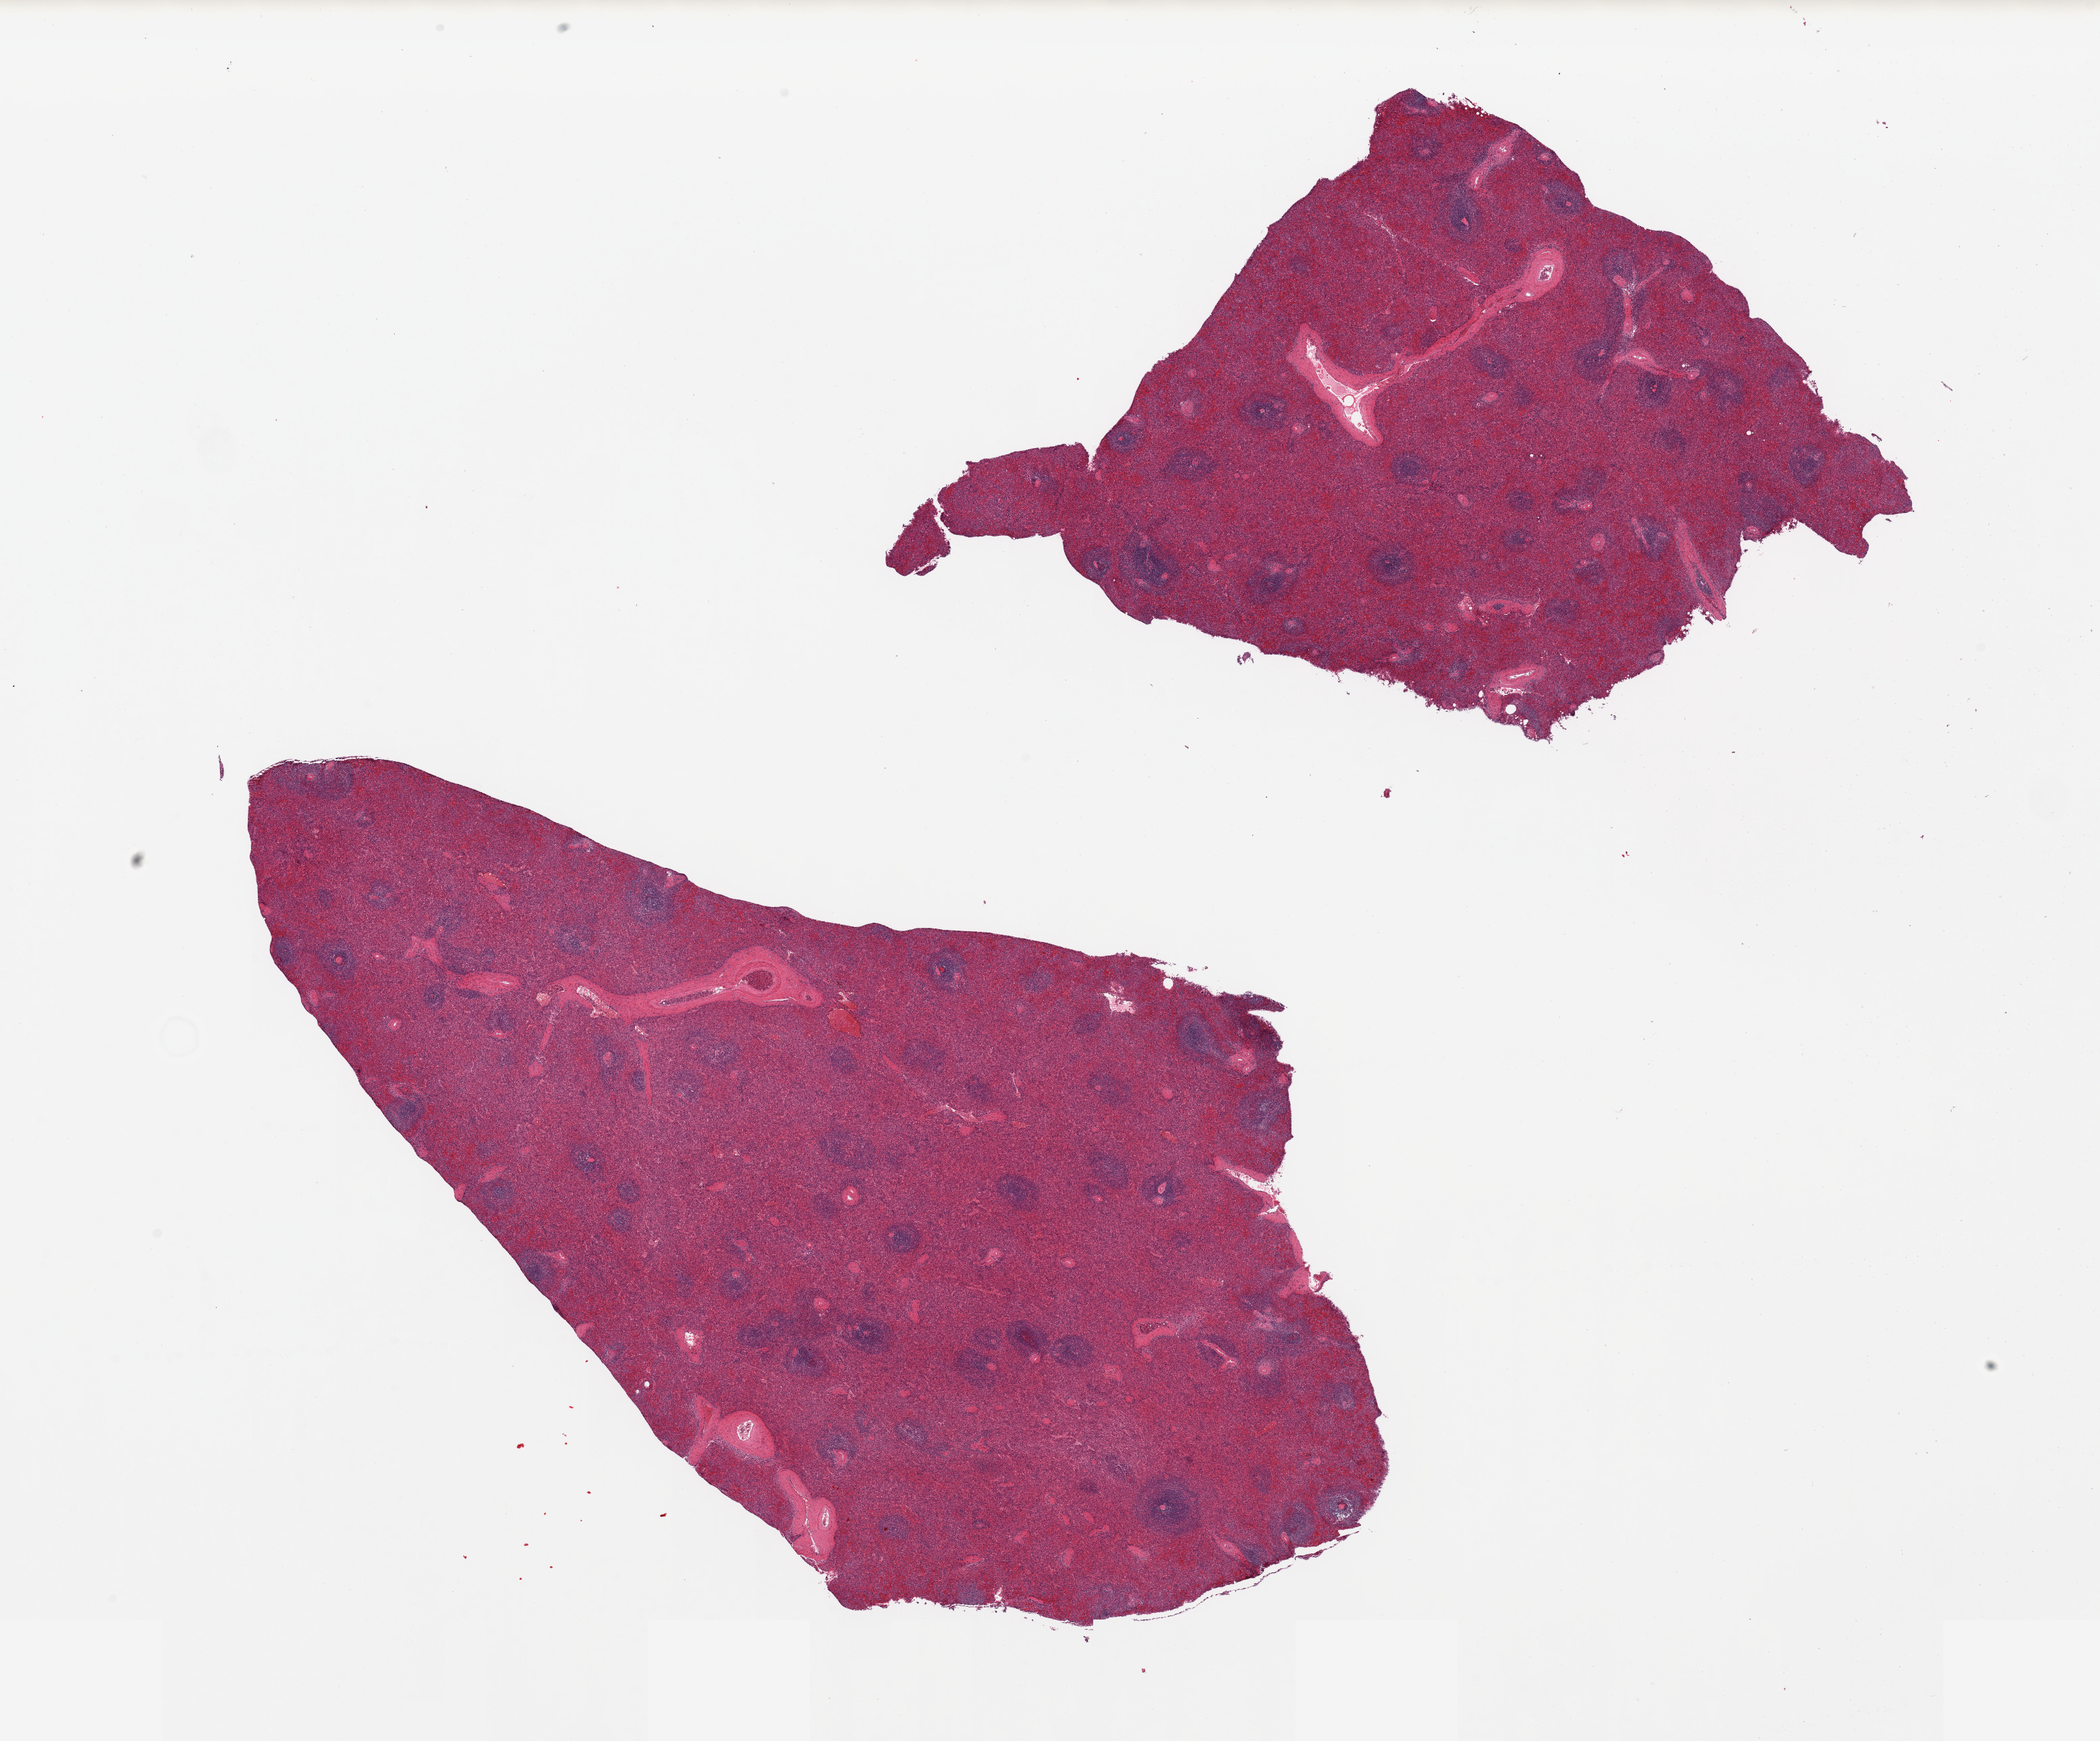
H&E whole-slide image, brightfield, shown as a low-resolution overview of the whole scanned area (about 24.6 x 20.4 mm), PAXgene-fixed, paraffin-embedded tissue, target tissue: spleen, donor tissue sample.
Reviewer comment on this tissue sample: 2 pieces, congested.